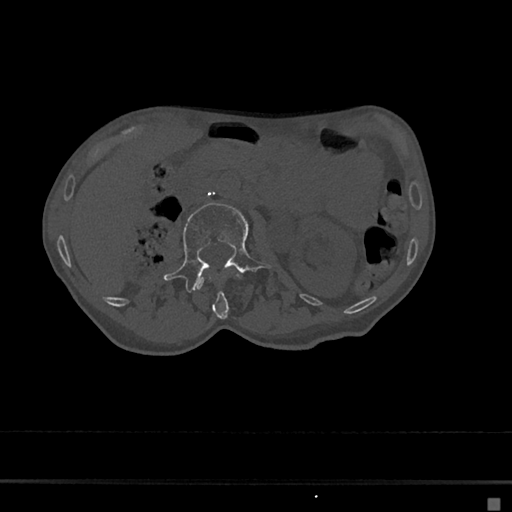
CT including the spine, one axial slice; position 24 of 797 along the scan axis; bone window (W 1800 / L 400 HU); 0.5 mm slice thickness; 512 × 512 image matrix, field of view 360 × 360 mm. Female patient, age 68 years. Case-level facts recorded for this patient, not image findings: primary cancer: renal.
Annotated regions visible in this slice (semi-automatically segmented with operator editing):
- L1 vertebra: bounding box <197,271,241,319> (left, top, right, bottom; pixels)
- L2 vertebra: <164,203,273,293>